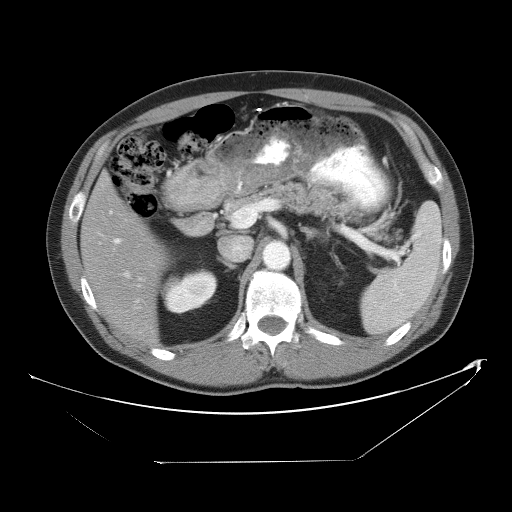
Contrast-enhanced abdominal CT, one axial slice; slice 29 of 53 in the series (ordered by position); reconstruction kernel STANDARD; intravenous contrast given; soft-tissue window (W 400 / L 40 HU); 5 mm slice thickness; 512 × 512 image matrix, field of view 438 × 438 mm. Male patient, age 59 years. From the clinical record (not read from this slice): diagnosis: colorectal cancer liver metastases, imaged before liver resection; multiple liver metastases: yes; largest metastasis: 8.5 cm; disease in both lobes: no.
Structures marked on this image (expert manual segmentation):
- hepatic veins: bounding box <109,211,130,277> (left, top, right, bottom; pixels)
- liver: <82,178,166,345>
- planned liver remnant (the part of the liver to remain after resection): <82,178,166,345>
- portal vein (with intrahepatic branches): <114,238,142,302>